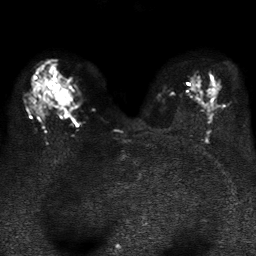
Breast MRI, one axial slice; position 22 of 37 along the scan axis; diffusion-weighted series; image 2 of 4 stored at this slice position (different b-values; order by instance number); 1.5 T; 5 mm slice thickness; 256 × 256 image matrix, field of view 320 × 320 mm. Female patient.
Annotated regions visible in this slice (expert manual segmentation):
- tumour on diffusion-weighted imaging: bounding box (x1, y1, x2, y2) in pixels: (56, 88, 70, 106)